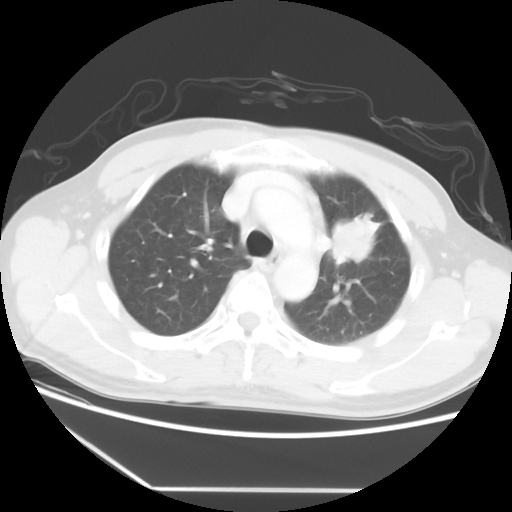
Chest CT, one axial slice. Position 41 of 56 along the scan axis. 120 kVp. Lung window (W 1500 / L -600 HU). 512 × 512 image matrix, field of view 373 × 373 mm. Male patient, age 53 years. From the clinical record (not read from this slice): clinical TNM (as recorded): T2a N1 M1b.
Structures marked on this image (rectangle marked by the reading radiologist):
- lung tumour (recorded histology: adenocarcinoma): bounding box <330,213,385,268> (left, top, right, bottom; pixels)